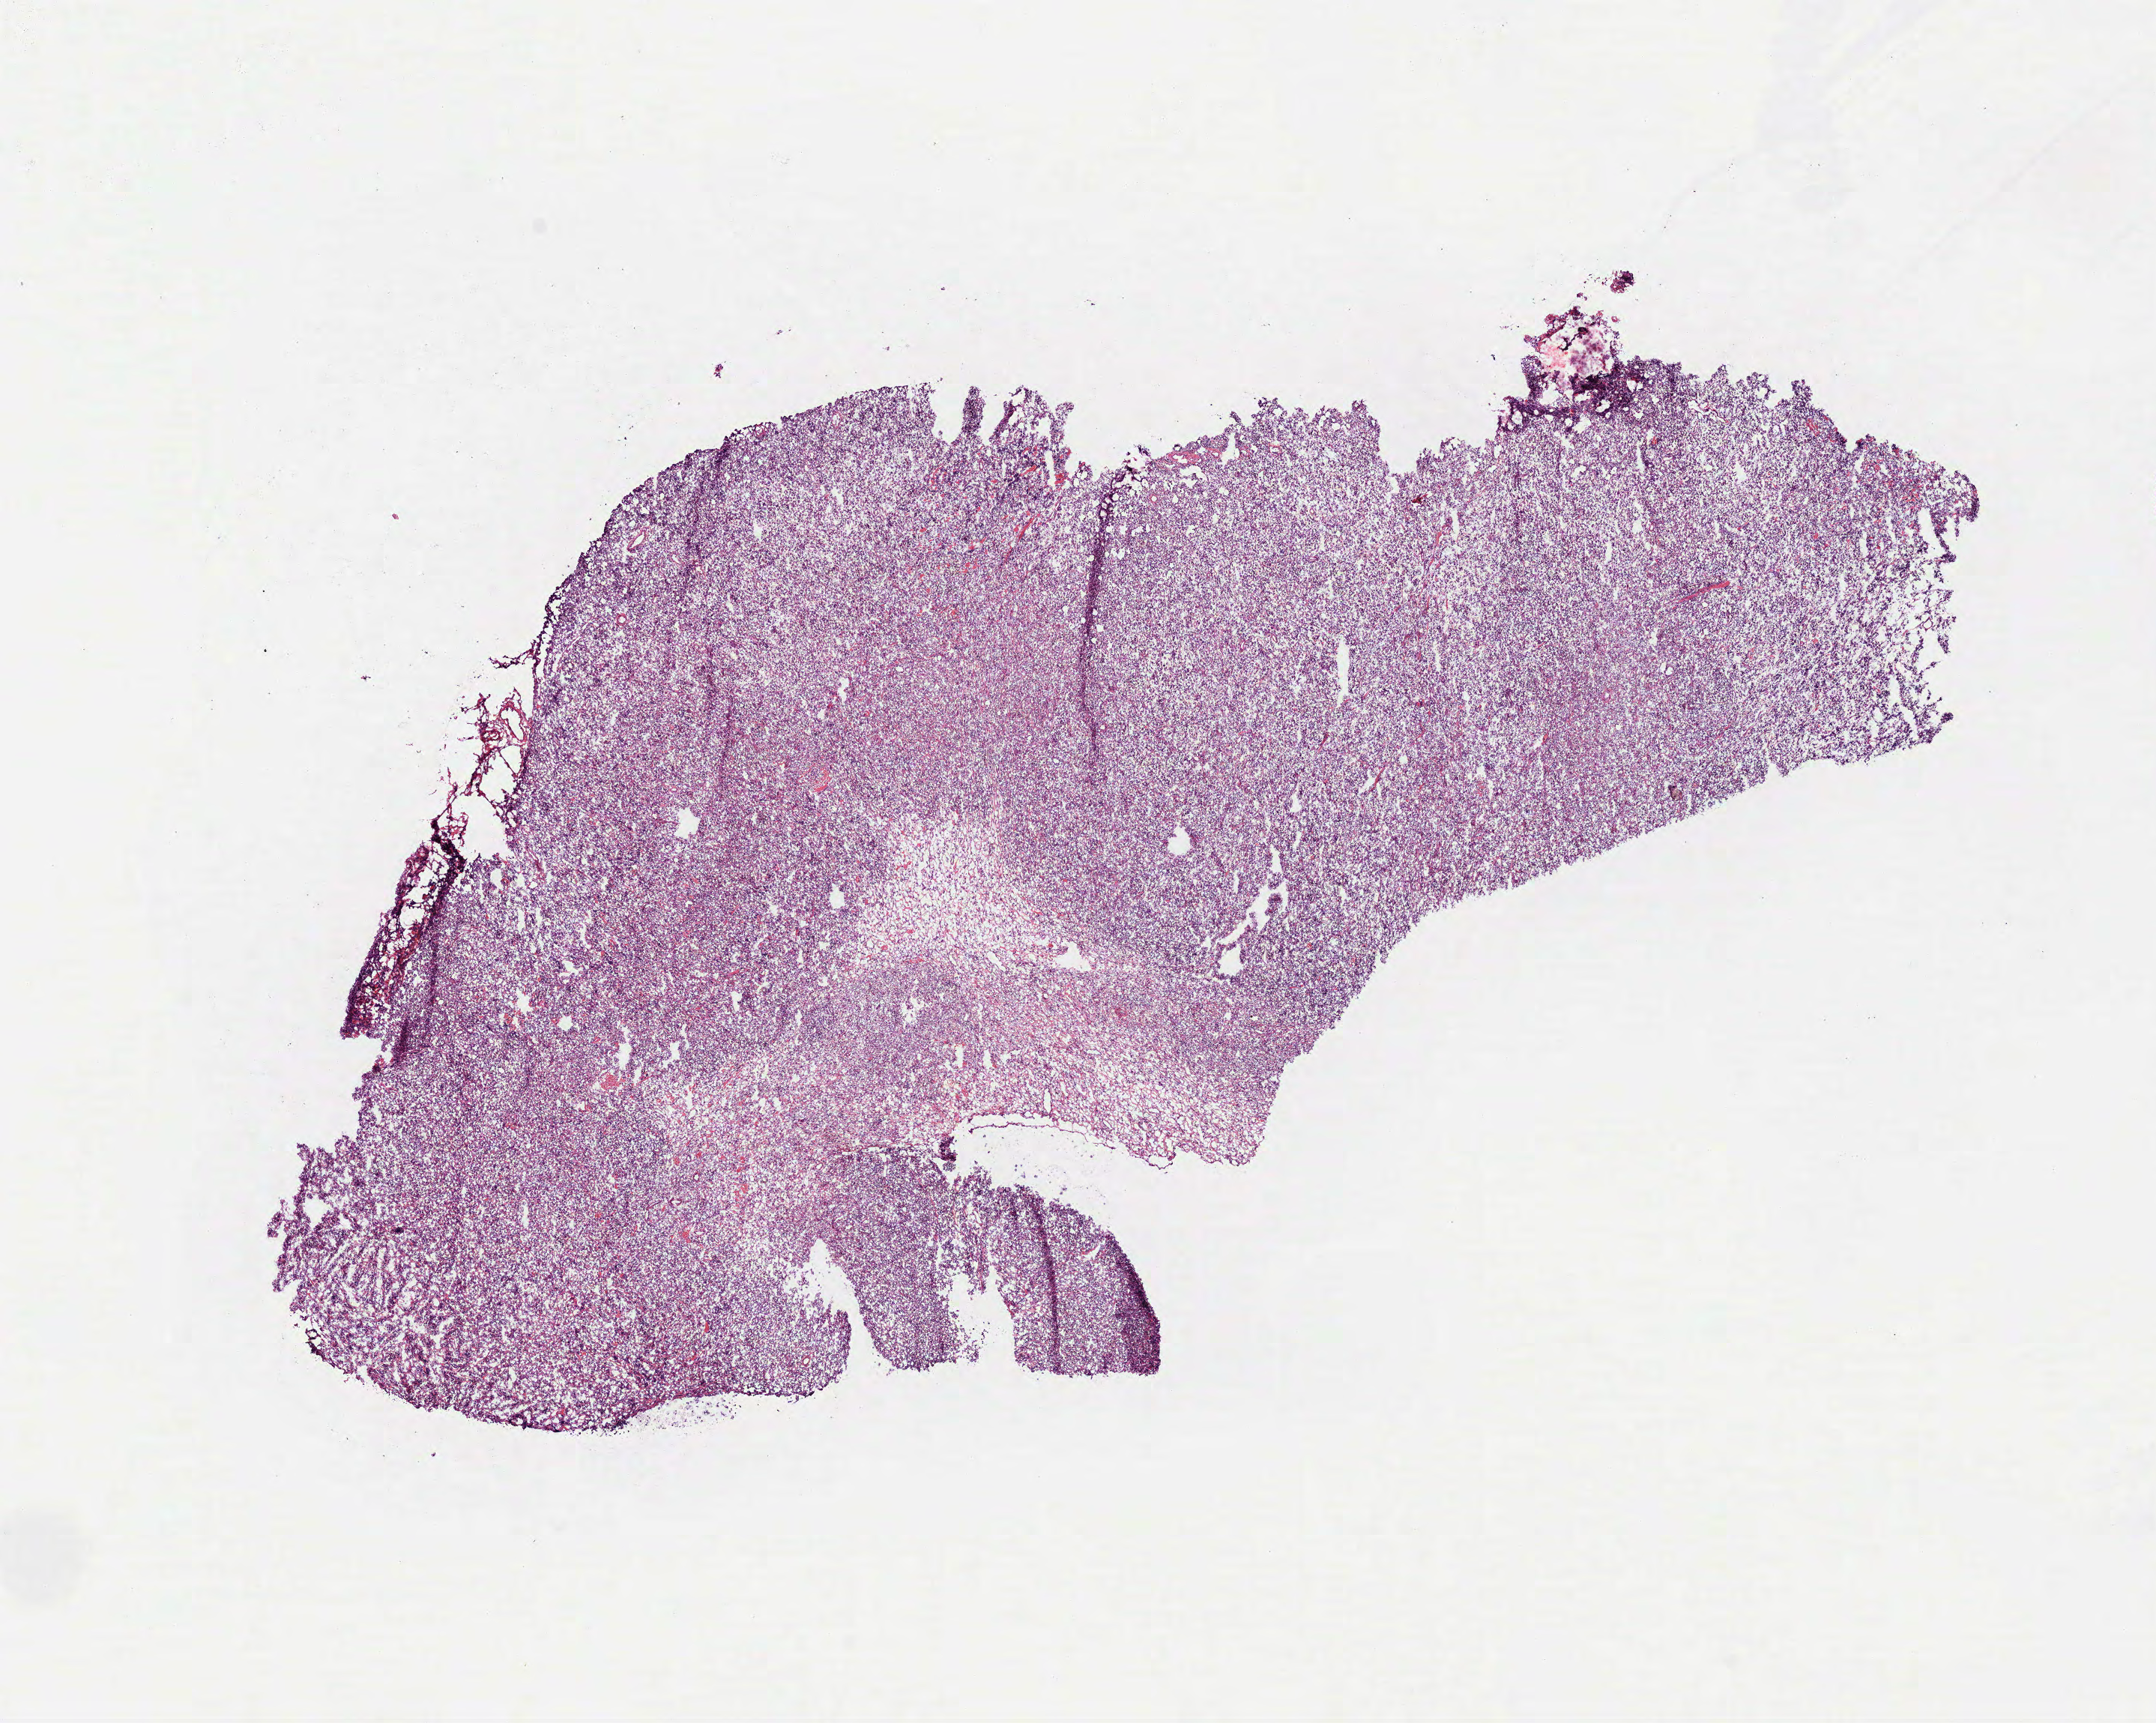
Digitized H&E-stained tissue section (whole slide), whole scanned area (about 11.6 x 9.3 mm) shown as a low-resolution overview; frozen section from the bottom of the tissue portion; lymphoid tissue, primary tumour sample. Male, age 67 years at initial diagnosis. Pathologist review of this section (percent, as recorded): tumour cells 100%, tumour nuclei 90%, normal cells 0%, stromal cells 0%, necrosis 0%. Infiltration values recorded for this section: lymphocyte infiltration 90%, monocyte infiltration 0%, neutrophil infiltration 0%.
Histologic diagnosis: Diffuse large B-cell lymphoma, NOS.